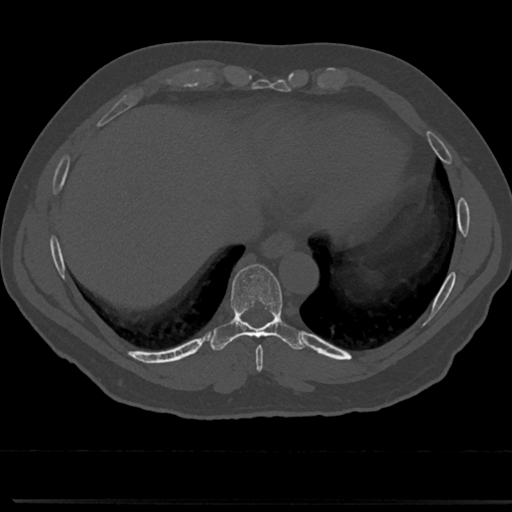
CT including the spine, one axial slice; reconstruction kernel Br40s/3; bone window (W 1800 / L 400 HU); 0.5 mm slice thickness; 512 × 512 image matrix. Male patient, age 61 years. Case-level facts recorded for this patient, not image findings: primary cancer: prostate.
Annotated regions visible in this slice (semi-automatically segmented with operator editing):
- T8 vertebra: bounding box <232,271,288,354> (left, top, right, bottom; pixels)
- T9 vertebra: <232,267,282,328>